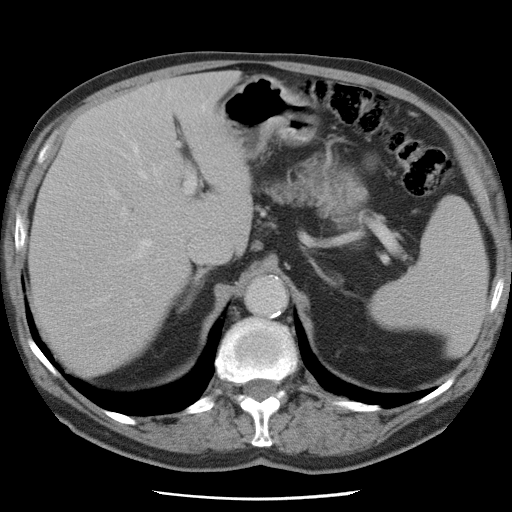
Contrast-enhanced abdominal CT, one axial slice. Slice 51 of 78 in the series (ordered by position). Soft-tissue window (W 400 / L 40 HU). 512 × 512 image matrix, field of view 337 × 337 mm. Male patient, age 75 years. Case-level facts recorded for this patient, not image findings: diagnosis: colorectal cancer liver metastases, imaged before liver resection; multiple liver metastases: yes; largest metastasis: 2.4 cm; disease in both lobes: yes.
Annotated regions visible in this slice (outlined manually by an expert reader):
- hepatic veins: bounding box (x1, y1, x2, y2) in pixels: (56, 103, 206, 261)
- liver: (30, 74, 251, 376)
- planned liver remnant (the part of the liver to remain after resection): (30, 125, 193, 377)
- portal vein (with intrahepatic branches): (109, 143, 196, 216)